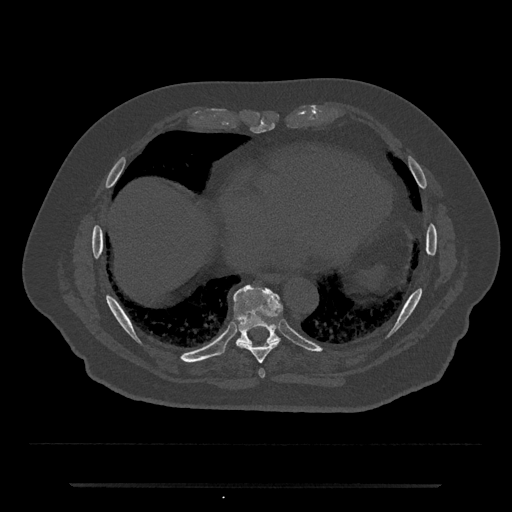
CT including the spine, one axial slice; slice 785 of 797 in the series (ordered by position); reconstruction kernel Br40s/3; bone window (W 1800 / L 400 HU); 0.5 mm slice thickness; 512 × 512 image matrix, field of view 434 × 434 mm. Male patient, age 80 years. From the clinical record (not read from this slice): primary cancer: prostate; vertebrae with lytic lesions (as recorded): L1, T11.
Outlined on this slice (semi-automatic segmentation, software-assisted and operator-edited):
- T8 vertebra: bounding box (x1, y1, x2, y2) in pixels: (237, 325, 279, 364)
- T9 vertebra: (220, 285, 282, 354)